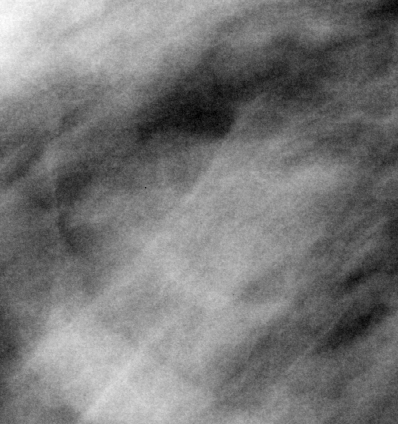
Cropped region of a digitized screen-film mammogram centred on a radiologist-marked abnormality; right breast; MLO view.
- Finding: mass, shape lobulated, margins obscured; BI-RADS assessment category 3; subtlety rating 3 on a 1 (subtle) to 5 (obvious) scale; benign; no additional work-up was recommended (benign without callback).